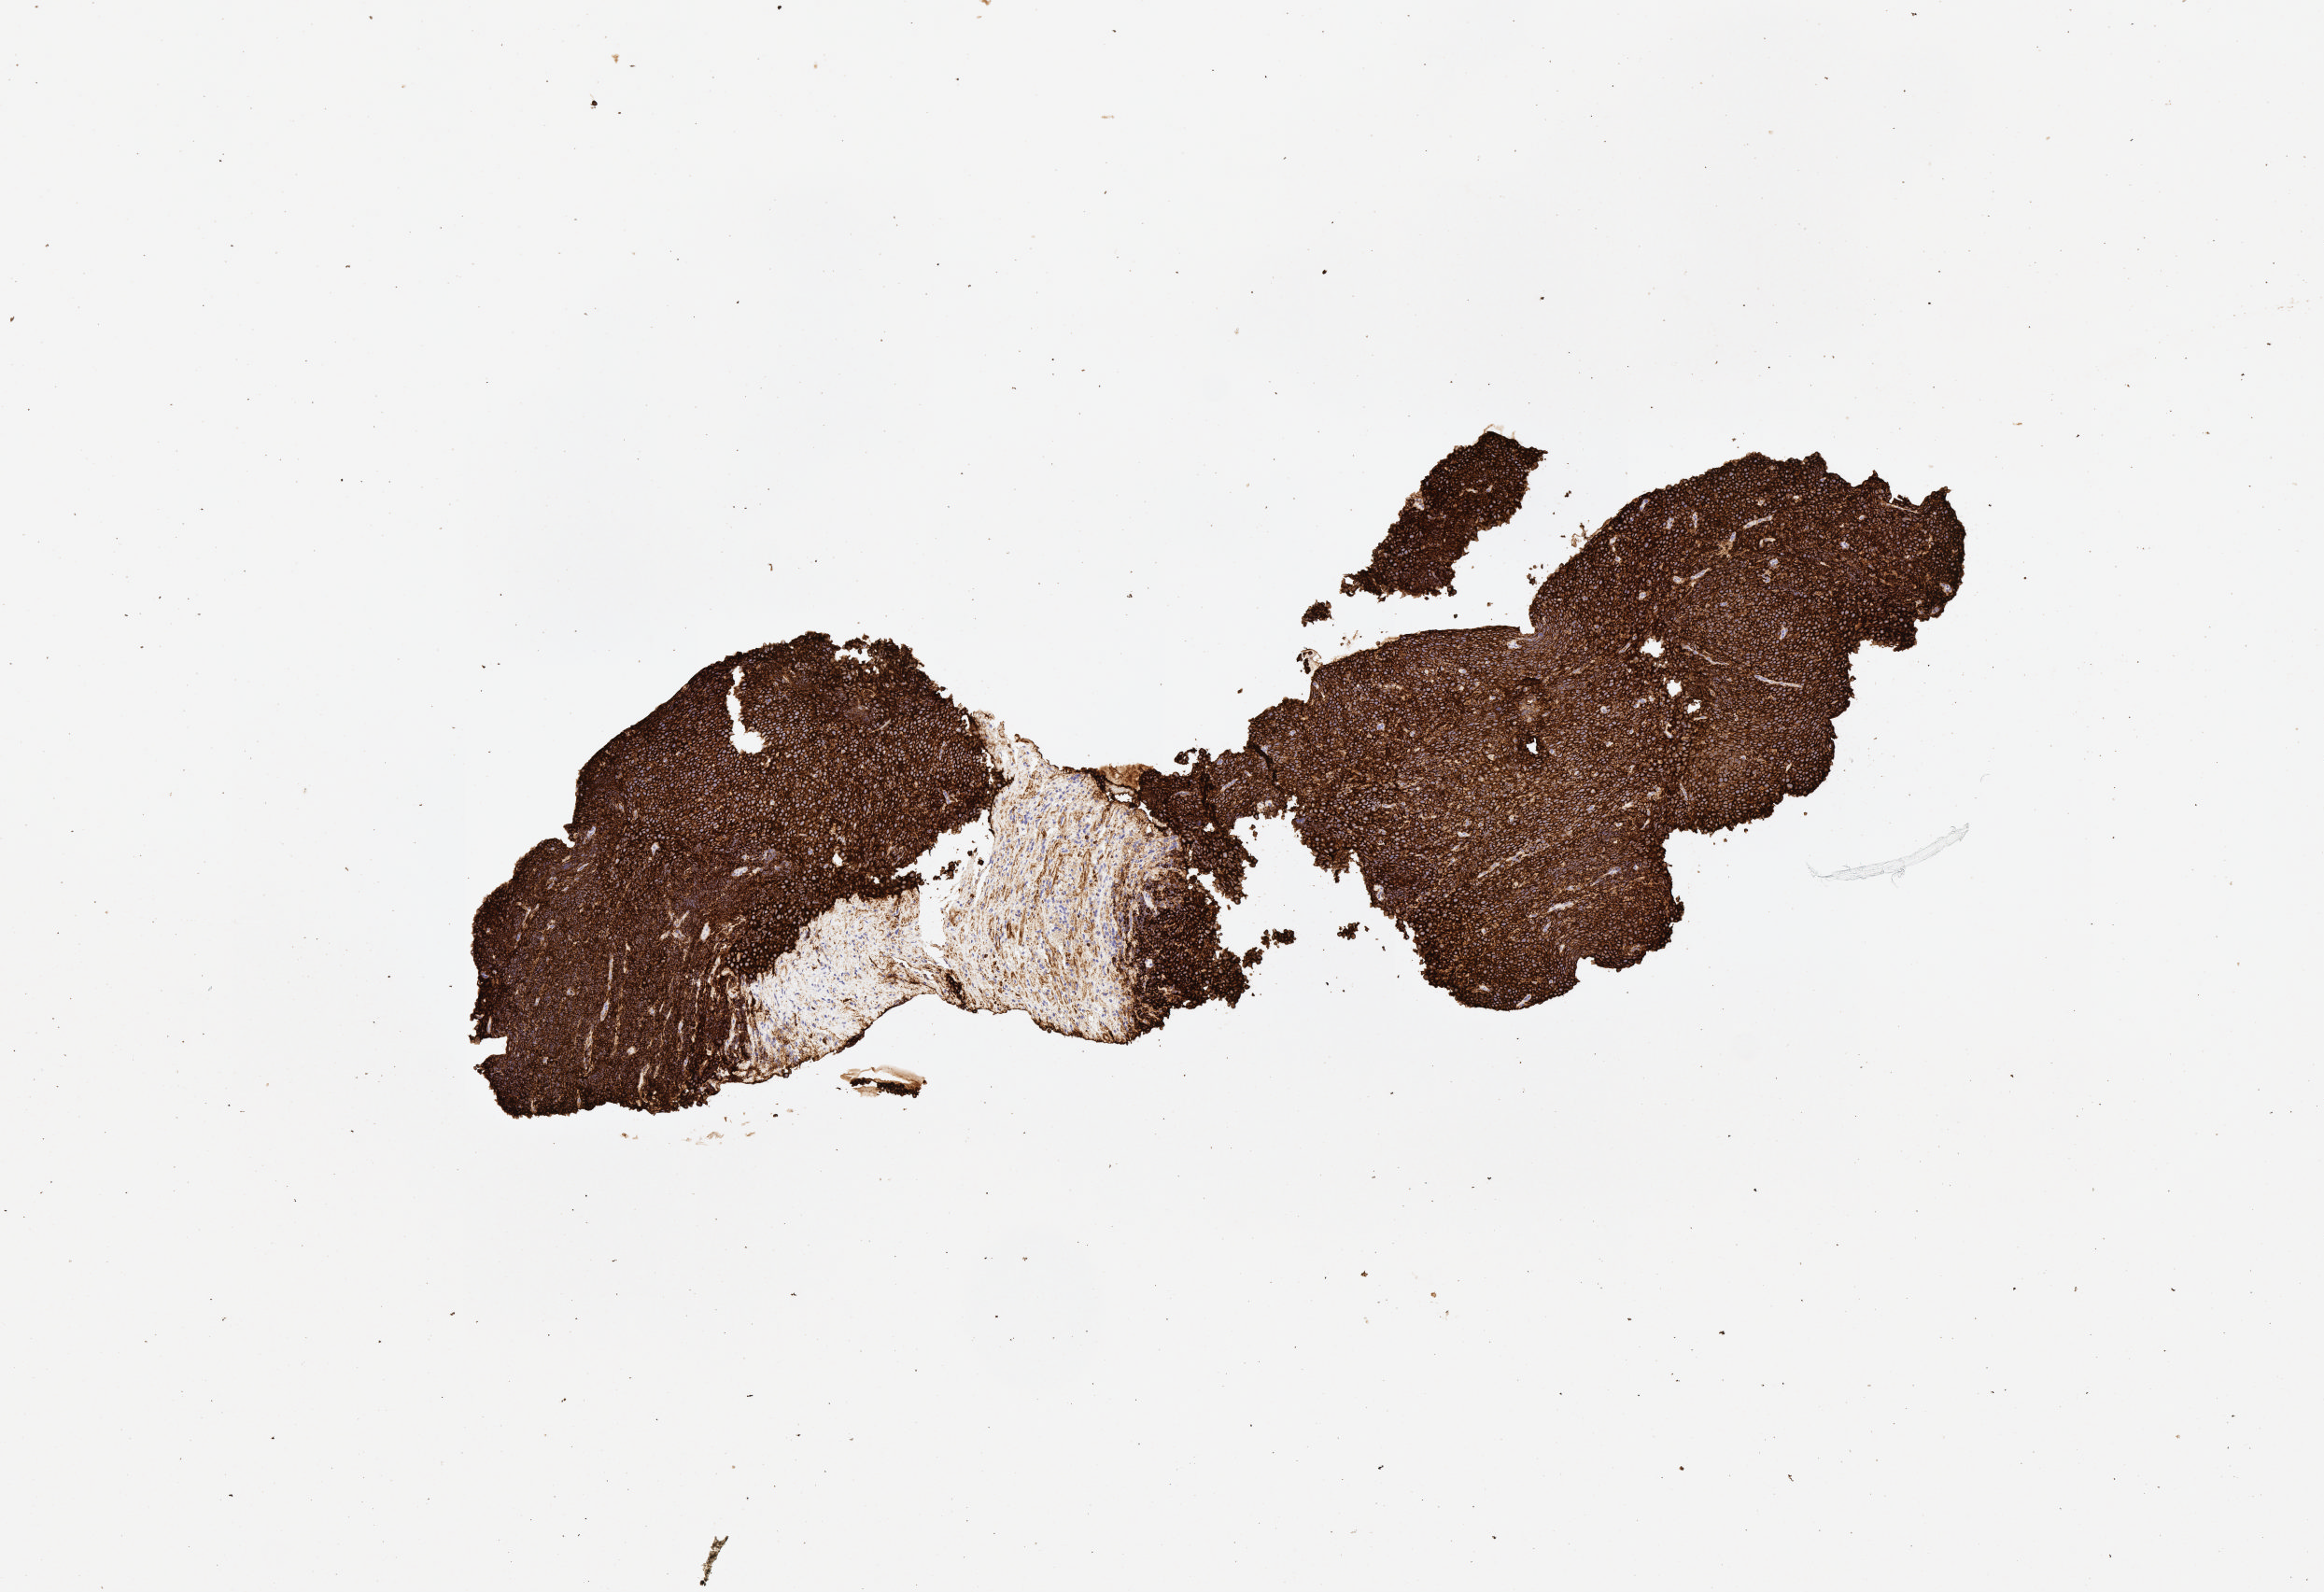
Whole-slide image, immunohistochemical stain for CD20, a low-resolution overview of the entire scanned area, about 5.0 x 3.4 mm. Specimen: tumor tissue. Male patient, age 15 years.
Diagnosis: Burkitt lymphoma, NOS.